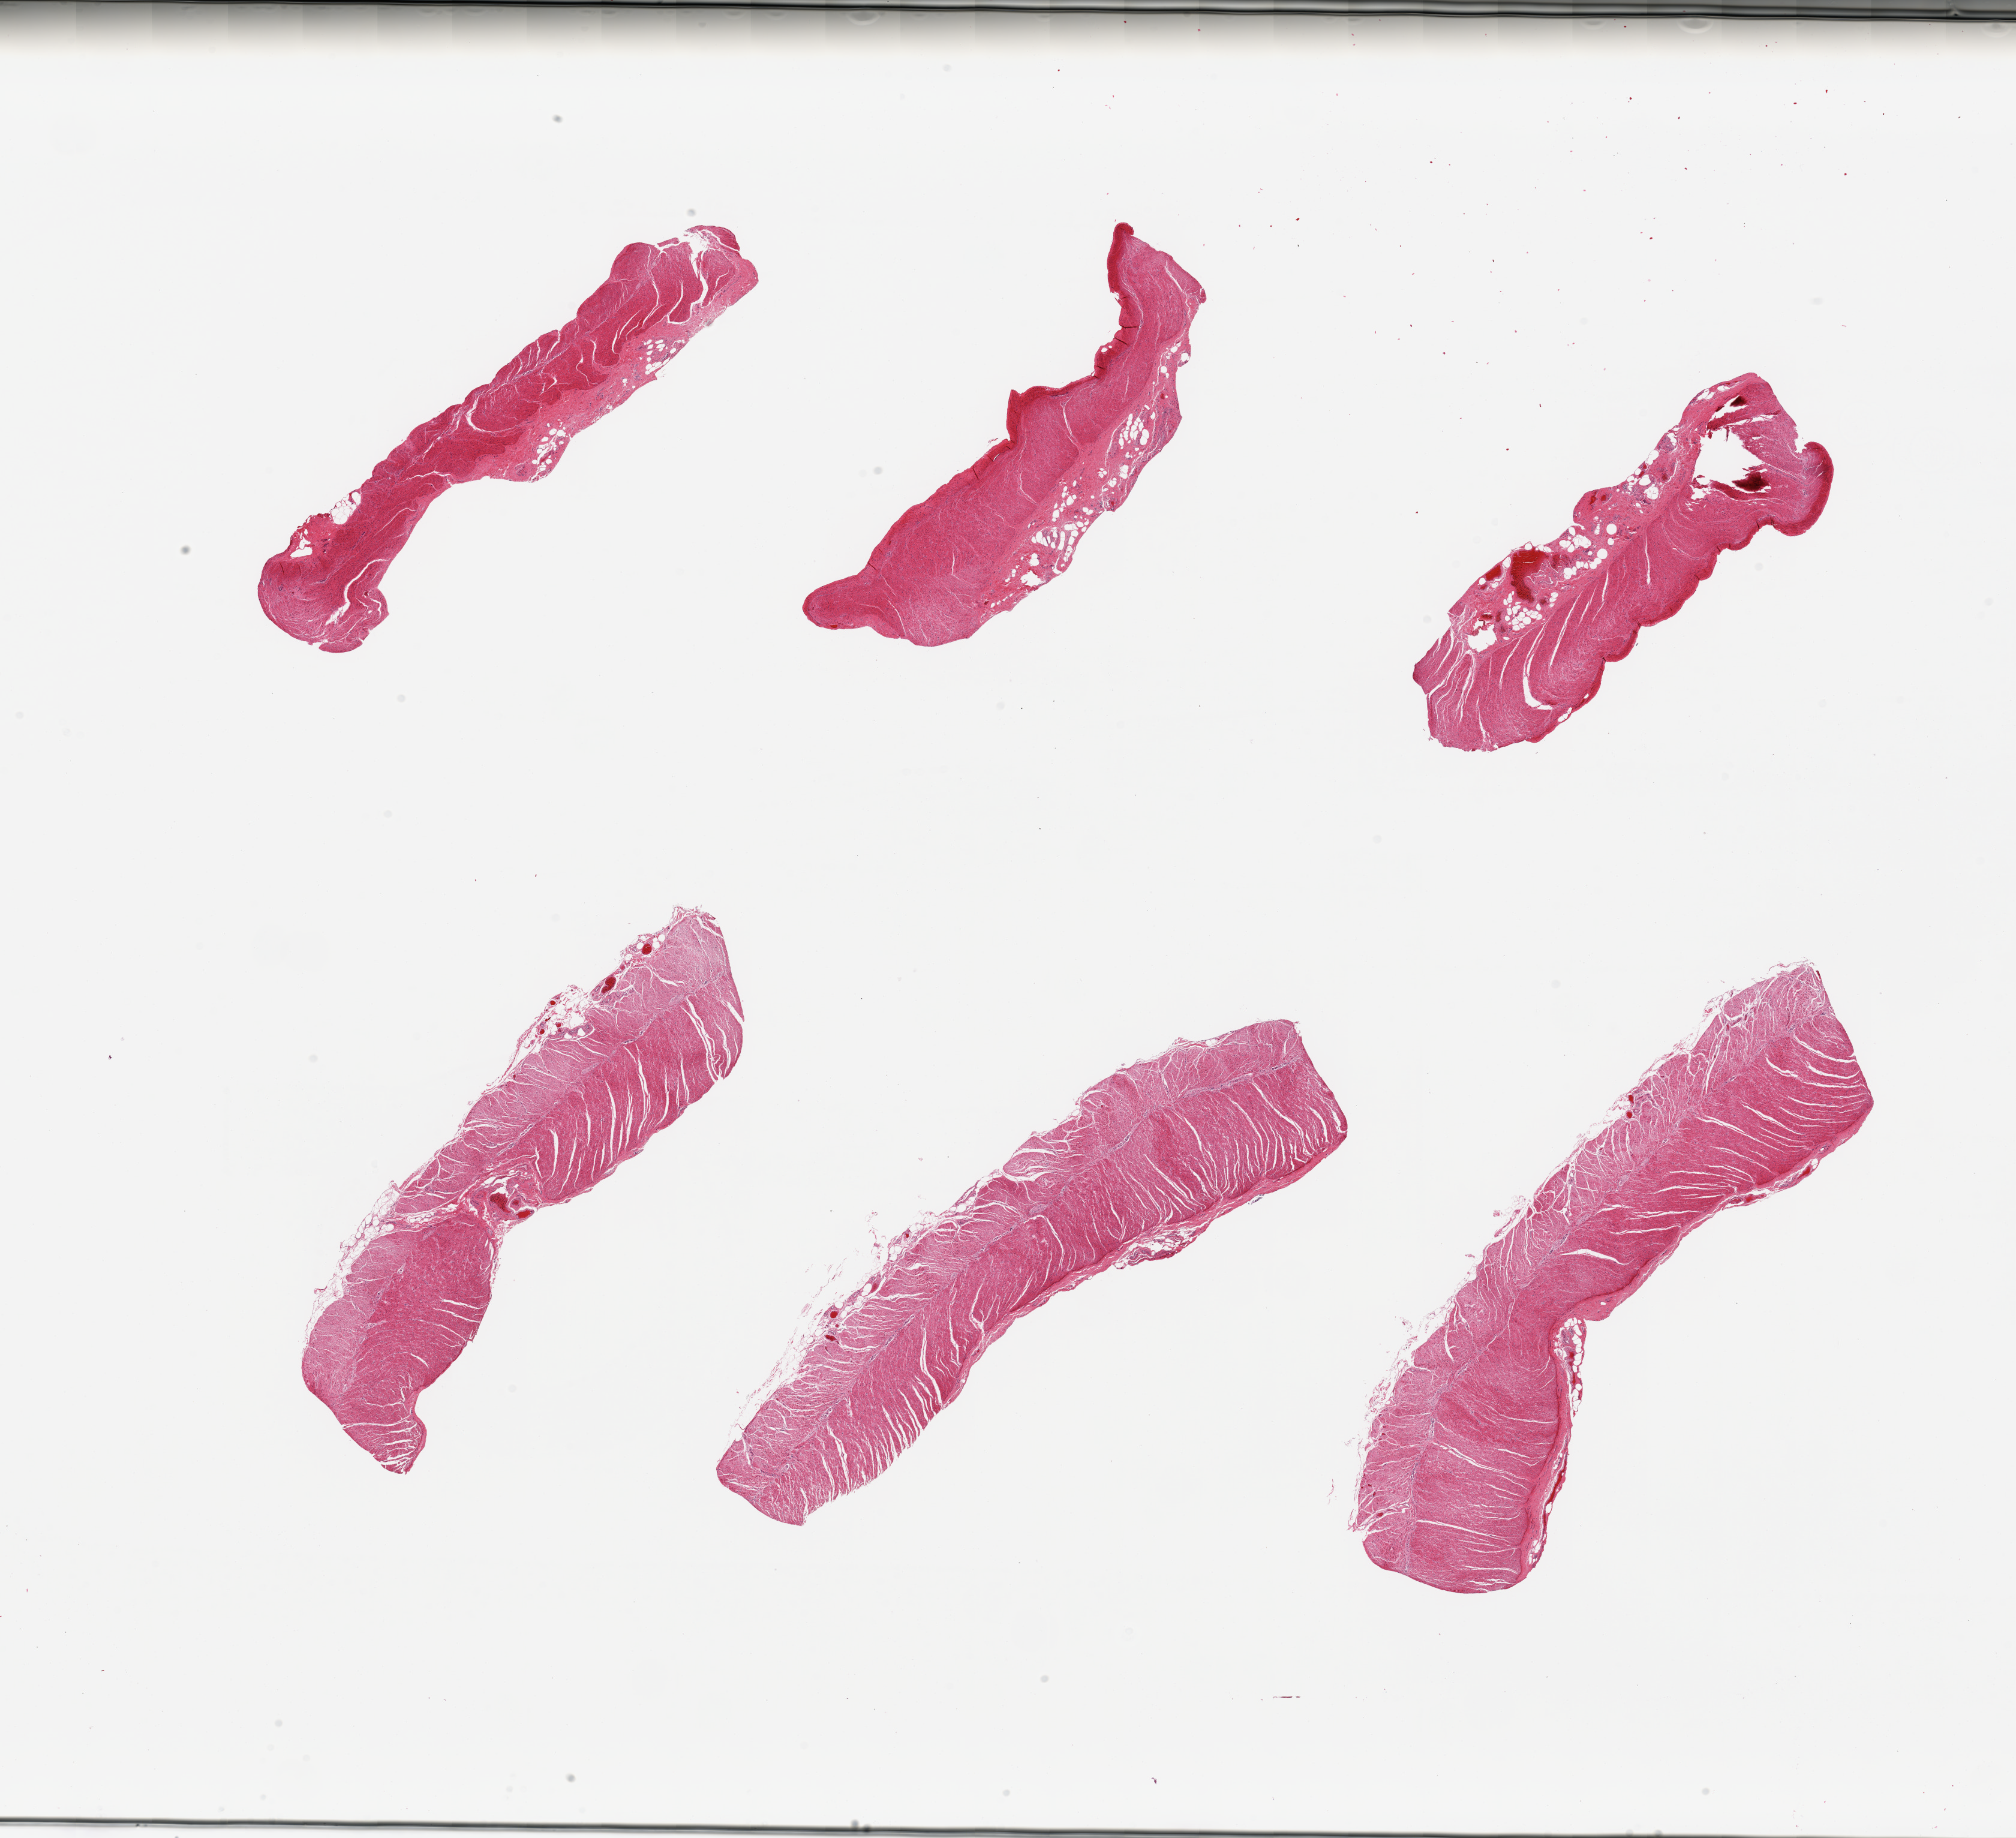
Digitized haematoxylin and eosin-stained section — whole scanned area (about 26.6 x 24.2 mm) shown as a low-resolution overview, PAXgene-fixed paraffin-embedded (PFPE) section, sampled site (target tissue): sigmoid colon, tissue donor sample. Donor: male.
* pathologist's review note for this sample: 6 pieces; well dissected